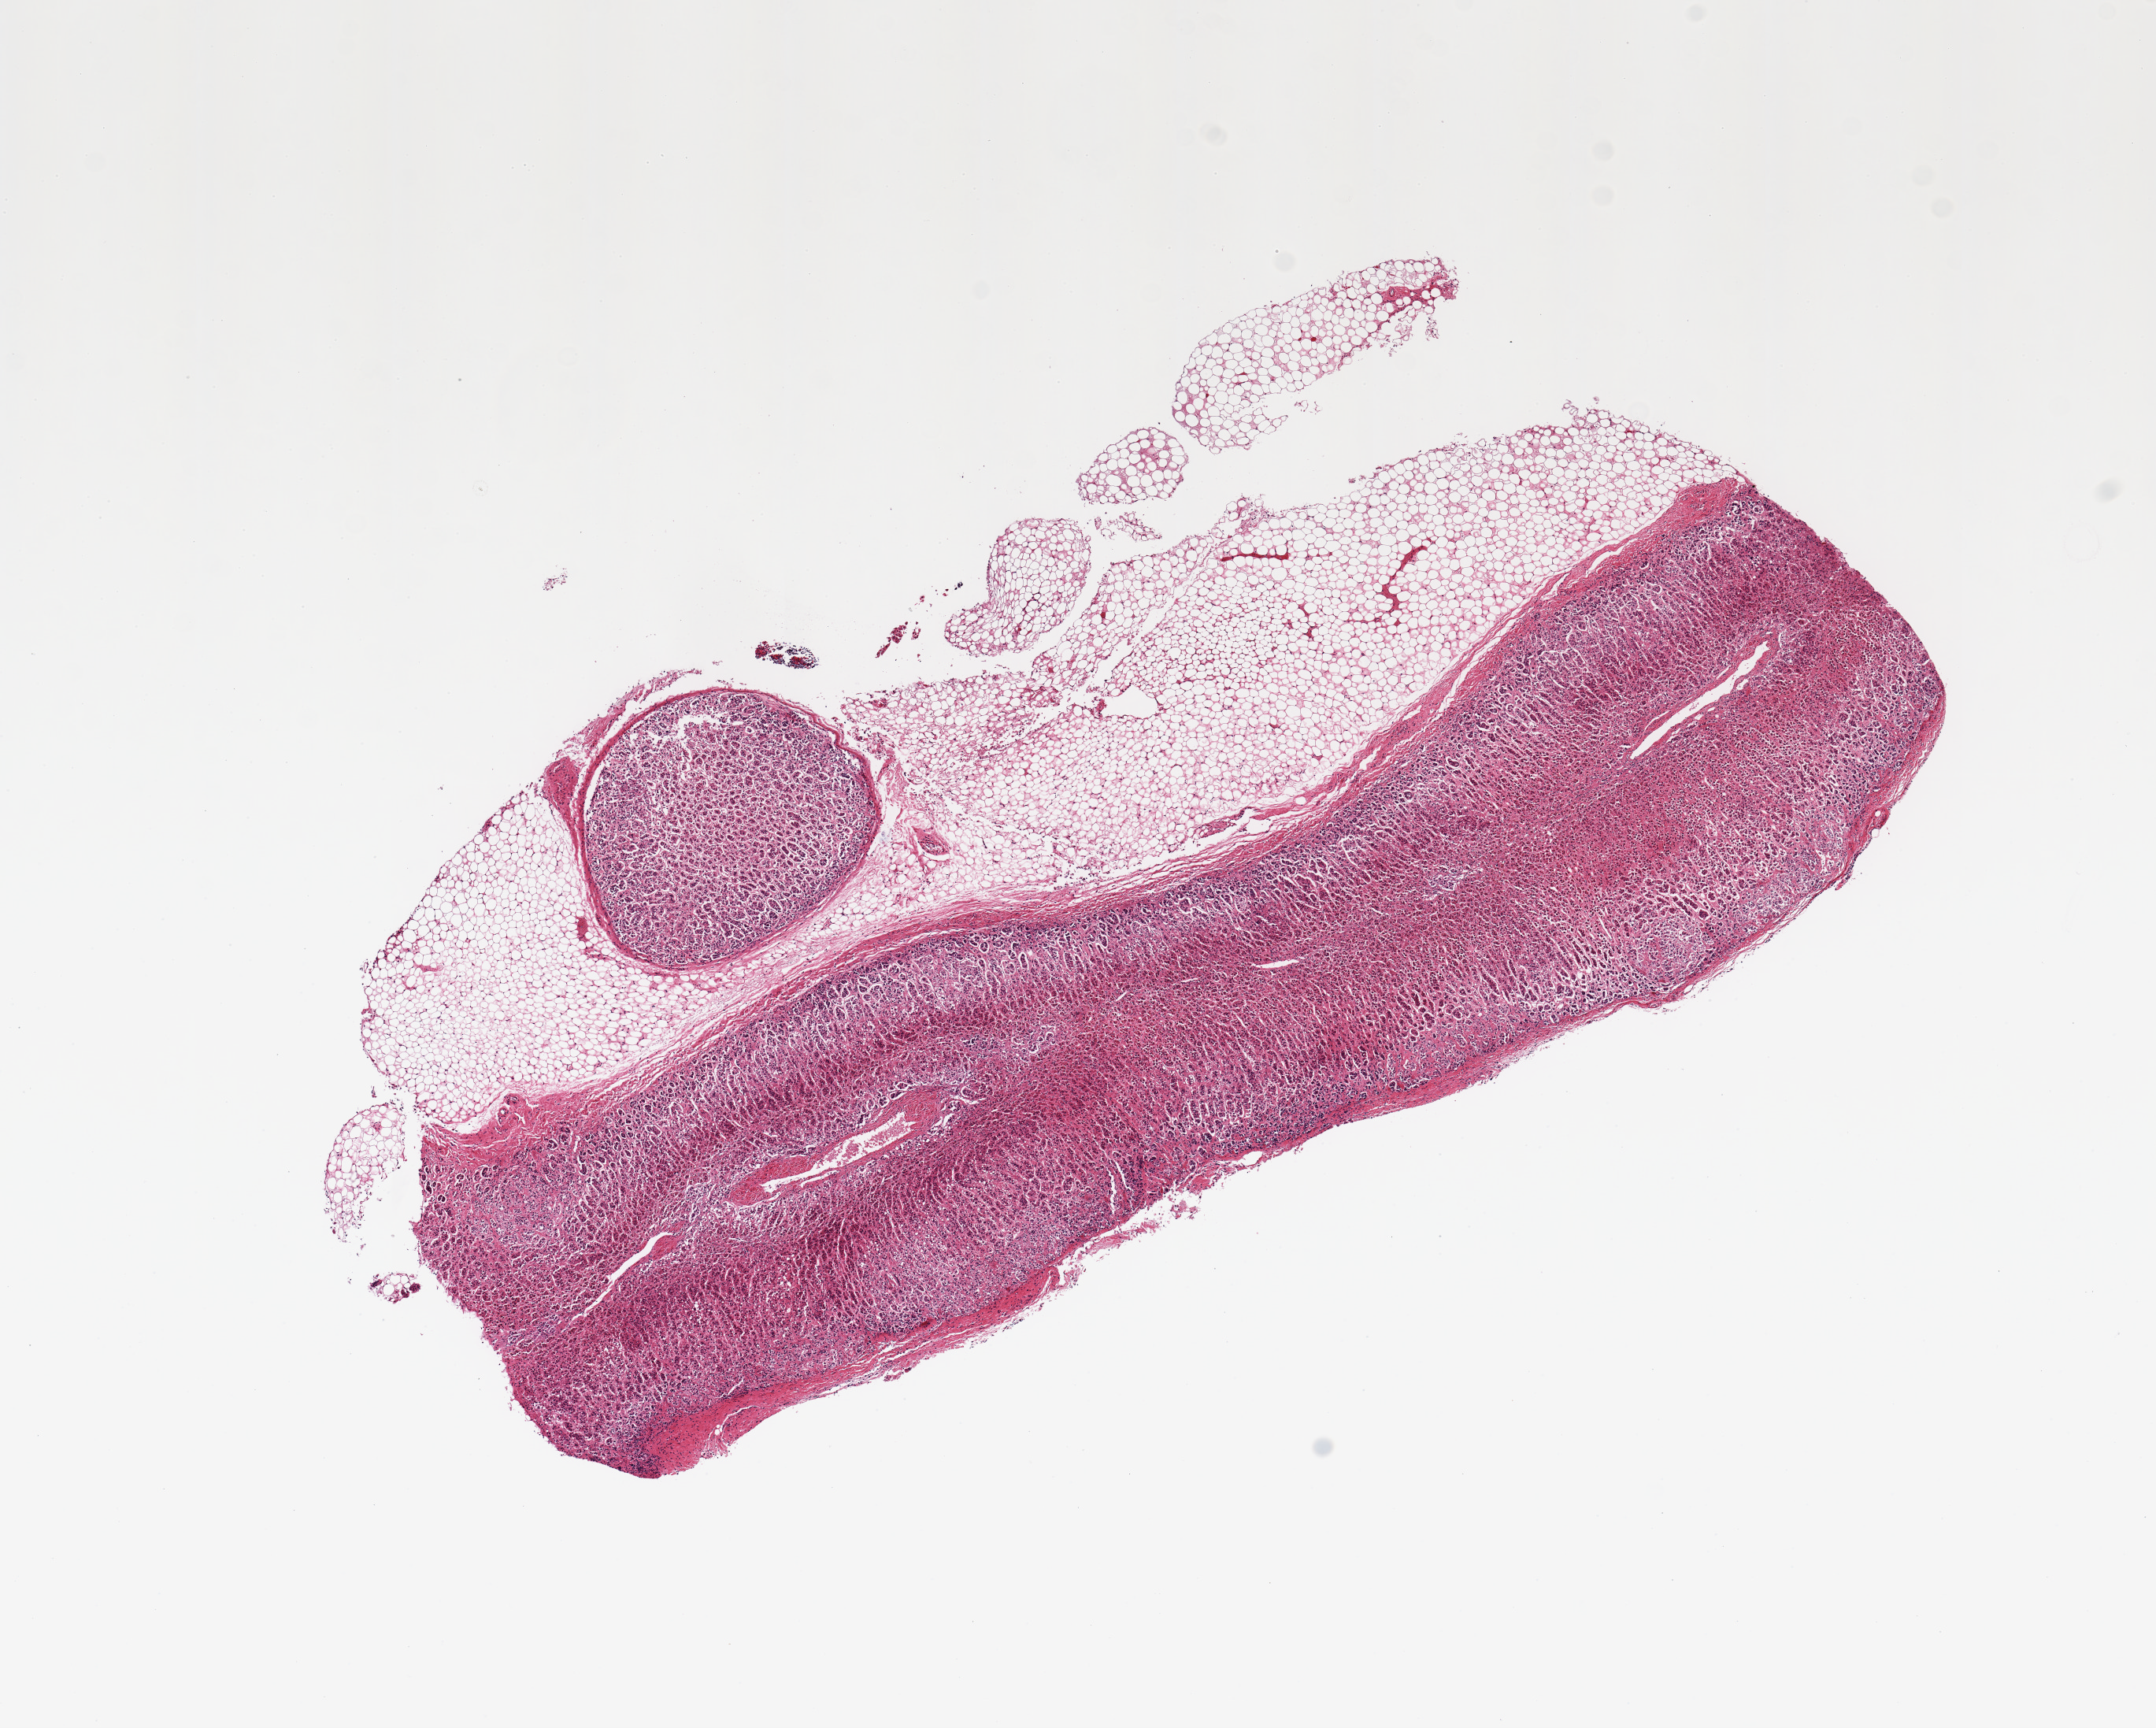
Whole-slide image, hematoxylin and eosin (H&E) stain — low-resolution overview of the scanned area, about 10.8 x 8.7 mm (slide scanned at 20x), PAXgene-fixed, paraffin-embedded tissue, section of adrenal gland (target tissue), donor tissue sample. Donor sex: female.
Reviewer comment on this tissue sample: 1 piece; adrenal with 30-40% attached fat.